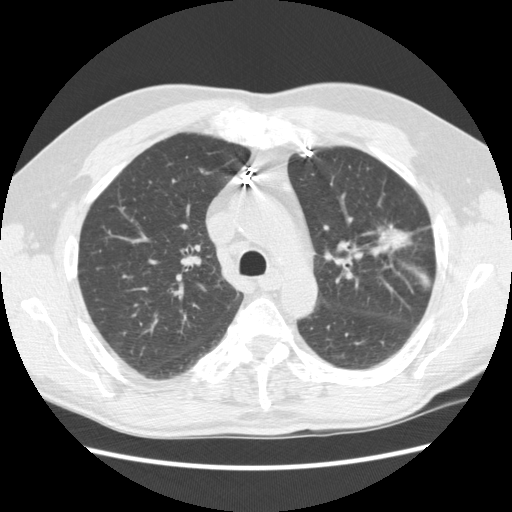
Axial slice from a low-dose chest CT screening exam. Baseline screening round. Lung window (W 1500 / L -600 HU). 2.5 mm slice thickness. Slice 167 of 231 in the series. 512 × 512 image matrix. Male participant, aged 72 years at enrolment. Former smoker at enrolment.
• Expert reader's lesion annotation, box from (x=360, y=212) to (x=428, y=260) px.
• Reader record for this screening exam (exam-level; its link to the box is not recorded): non-calcified nodule or mass ≥4 mm, left upper lobe, 25 × 18 mm, spiculated (stellate) margins, soft tissue attenuation.
• Official screen result: positive, change unspecified: nodule(s) >= 4 mm or enlarging nodule(s), mass(es), or other non-specific abnormalities suspicious for lung cancer.
• Later outcome: lung cancer diagnosed 35 days after this screen — adenocarcinoma, NOS, left upper lobe, well differentiated (G1), stage IIIB (AJCC 6th edition), 25 mm at pathology.